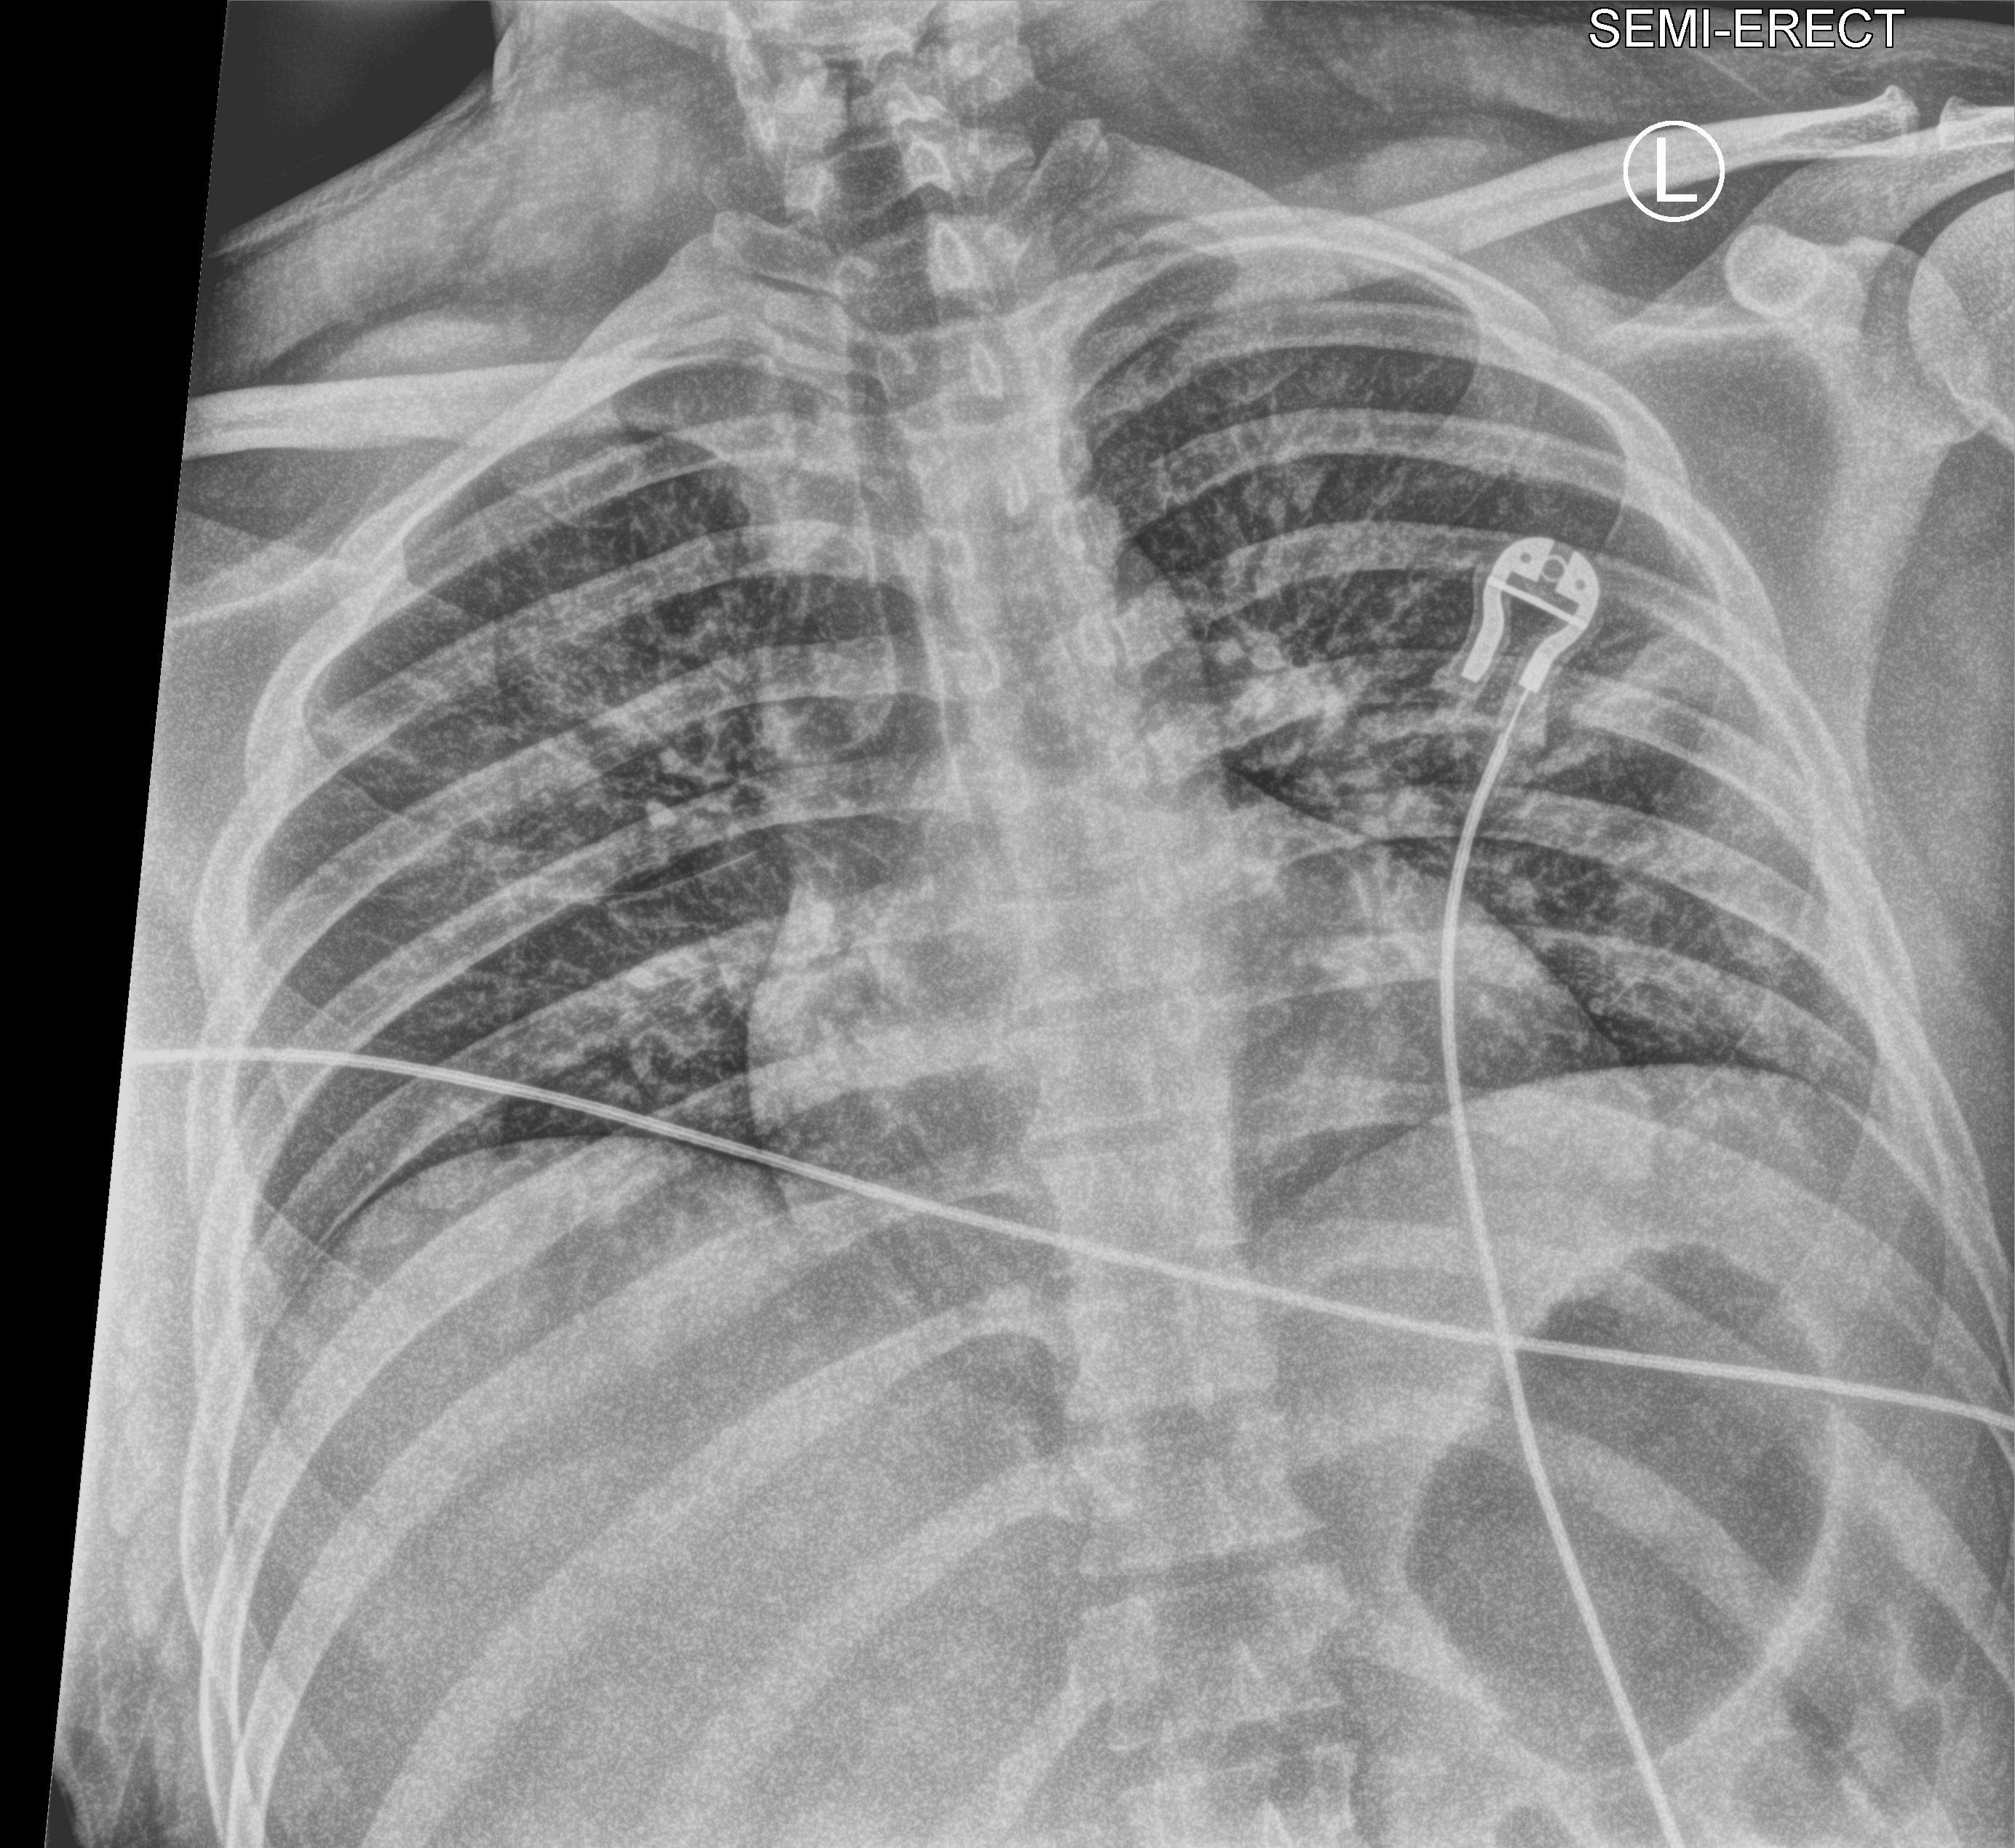
Portable chest radiograph. Patient hospitalised with COVID-19; male, aged 18–59 years.
Hospital-stay facts (about this admission, not read from this image; timing relative to this image not recorded): admitted to intensive care during this hospital stay: no.